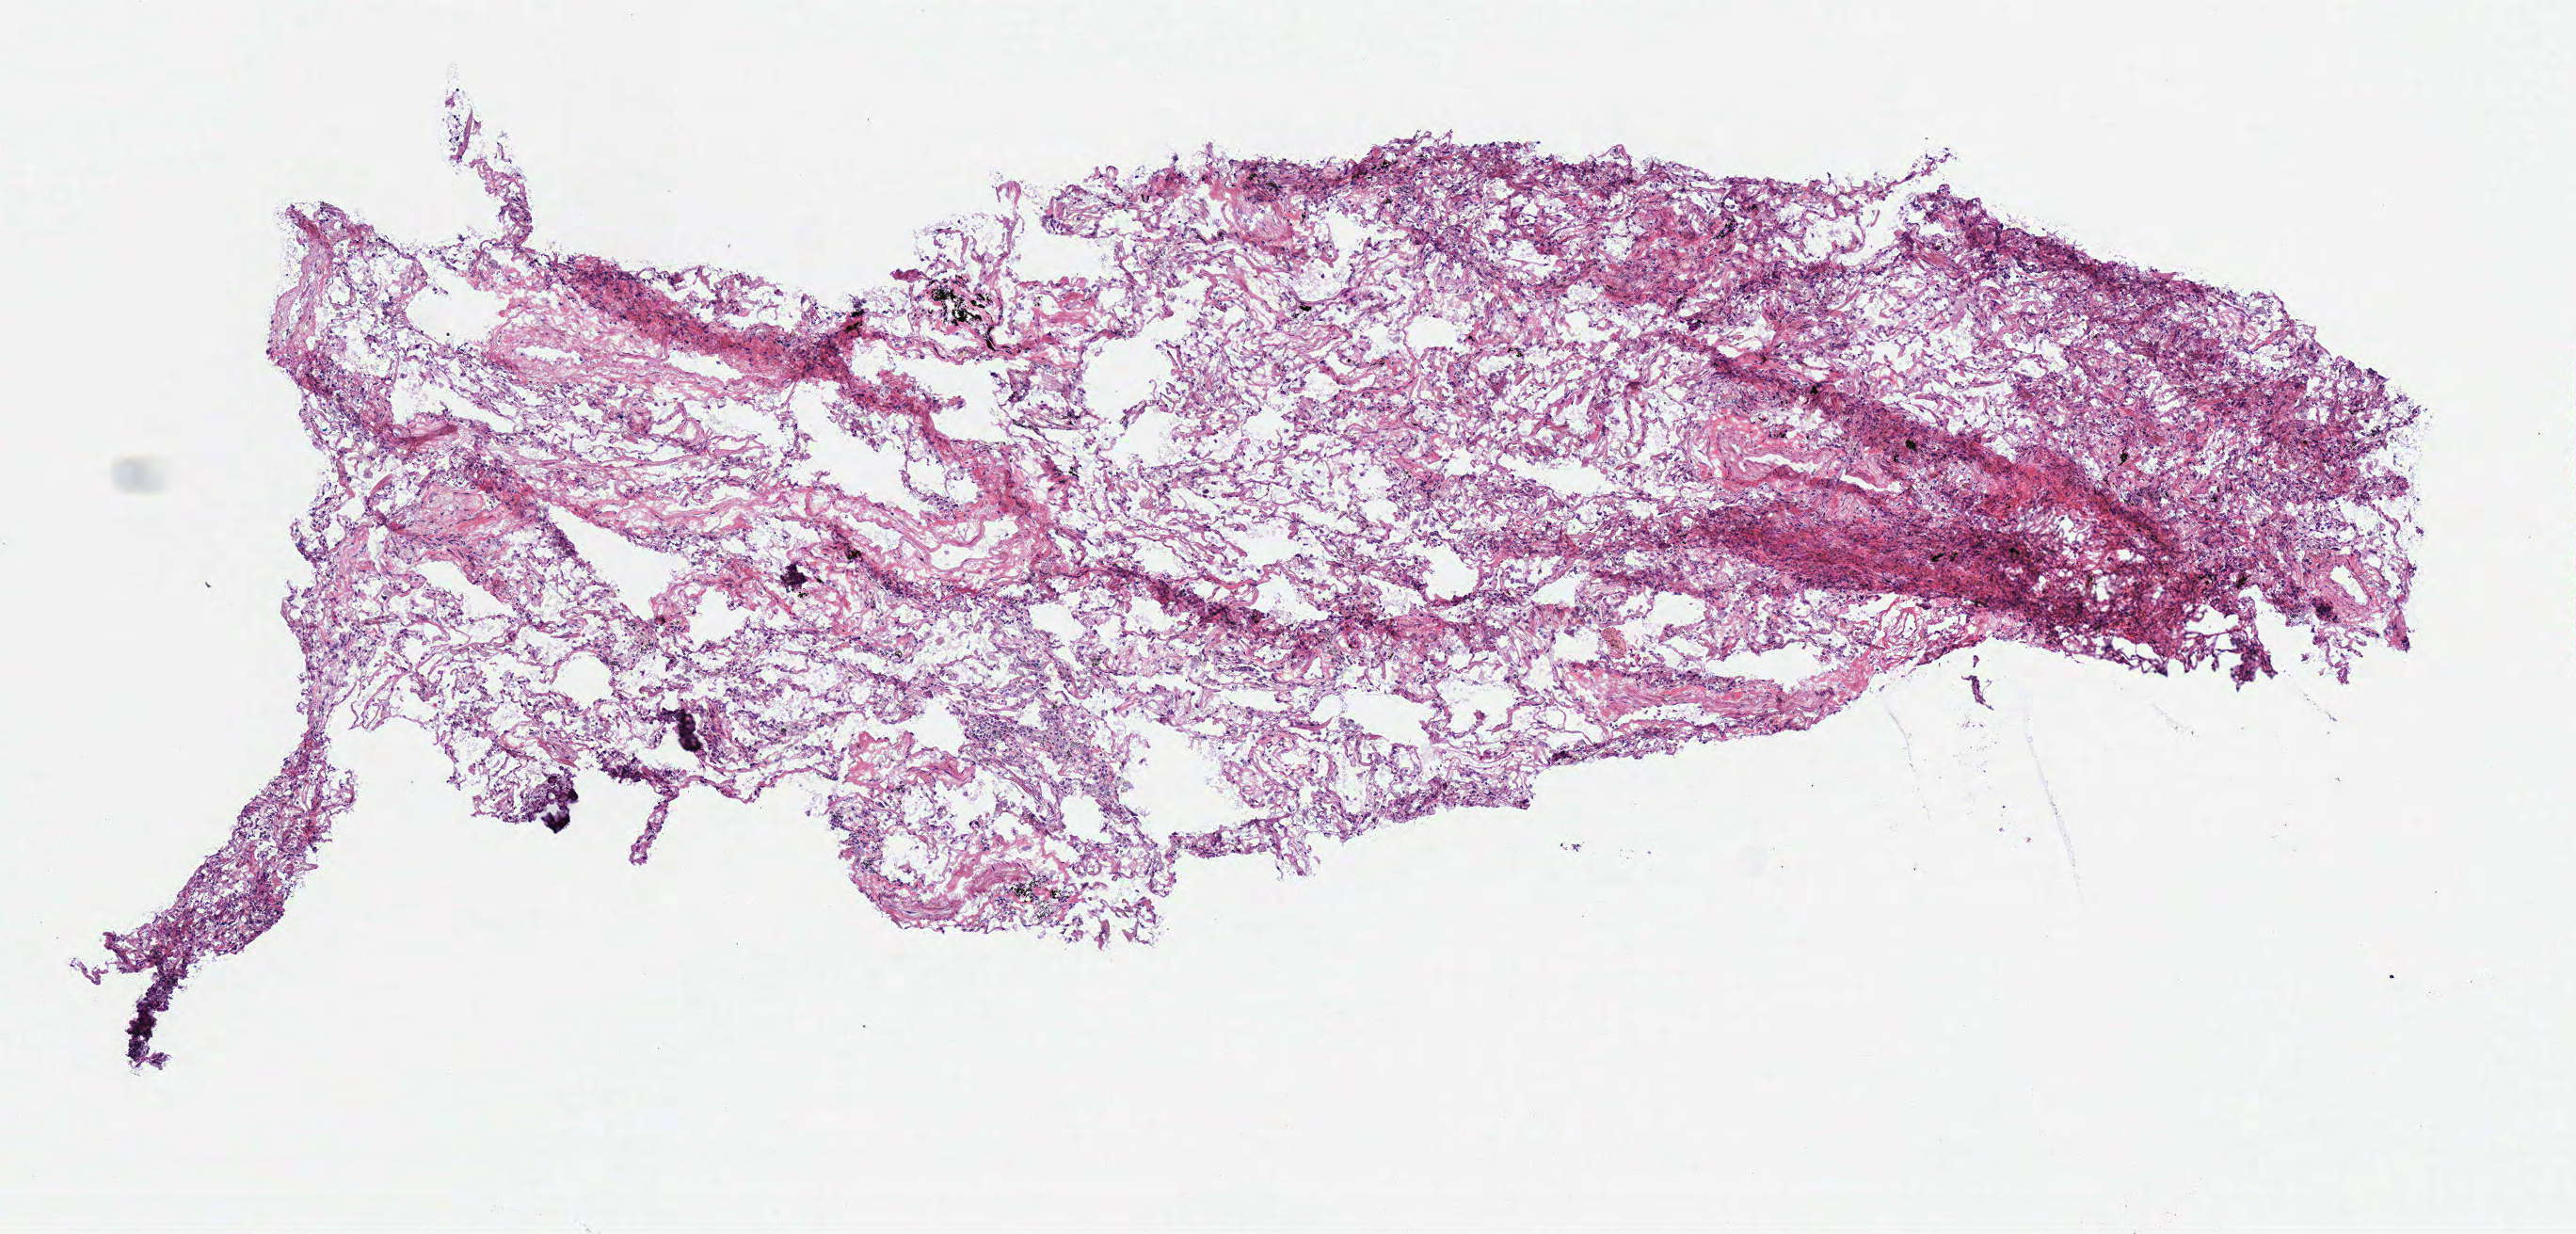
Digitized Hematoxylin and eosin (H&E) stained tissue section (whole slide) — a low-resolution overview of the entire scanned area, about 5.4 x 2.6 mm. Frozen section. Lung, solid tissue normal (non-tumour tissue) sample. Patient: female, age at initial diagnosis 72 years.
* this section: solid tissue normal (non-tumour) sample from the same patient
* patient diagnosis: Squamous cell carcinoma, NOS (upper lobe, lung)